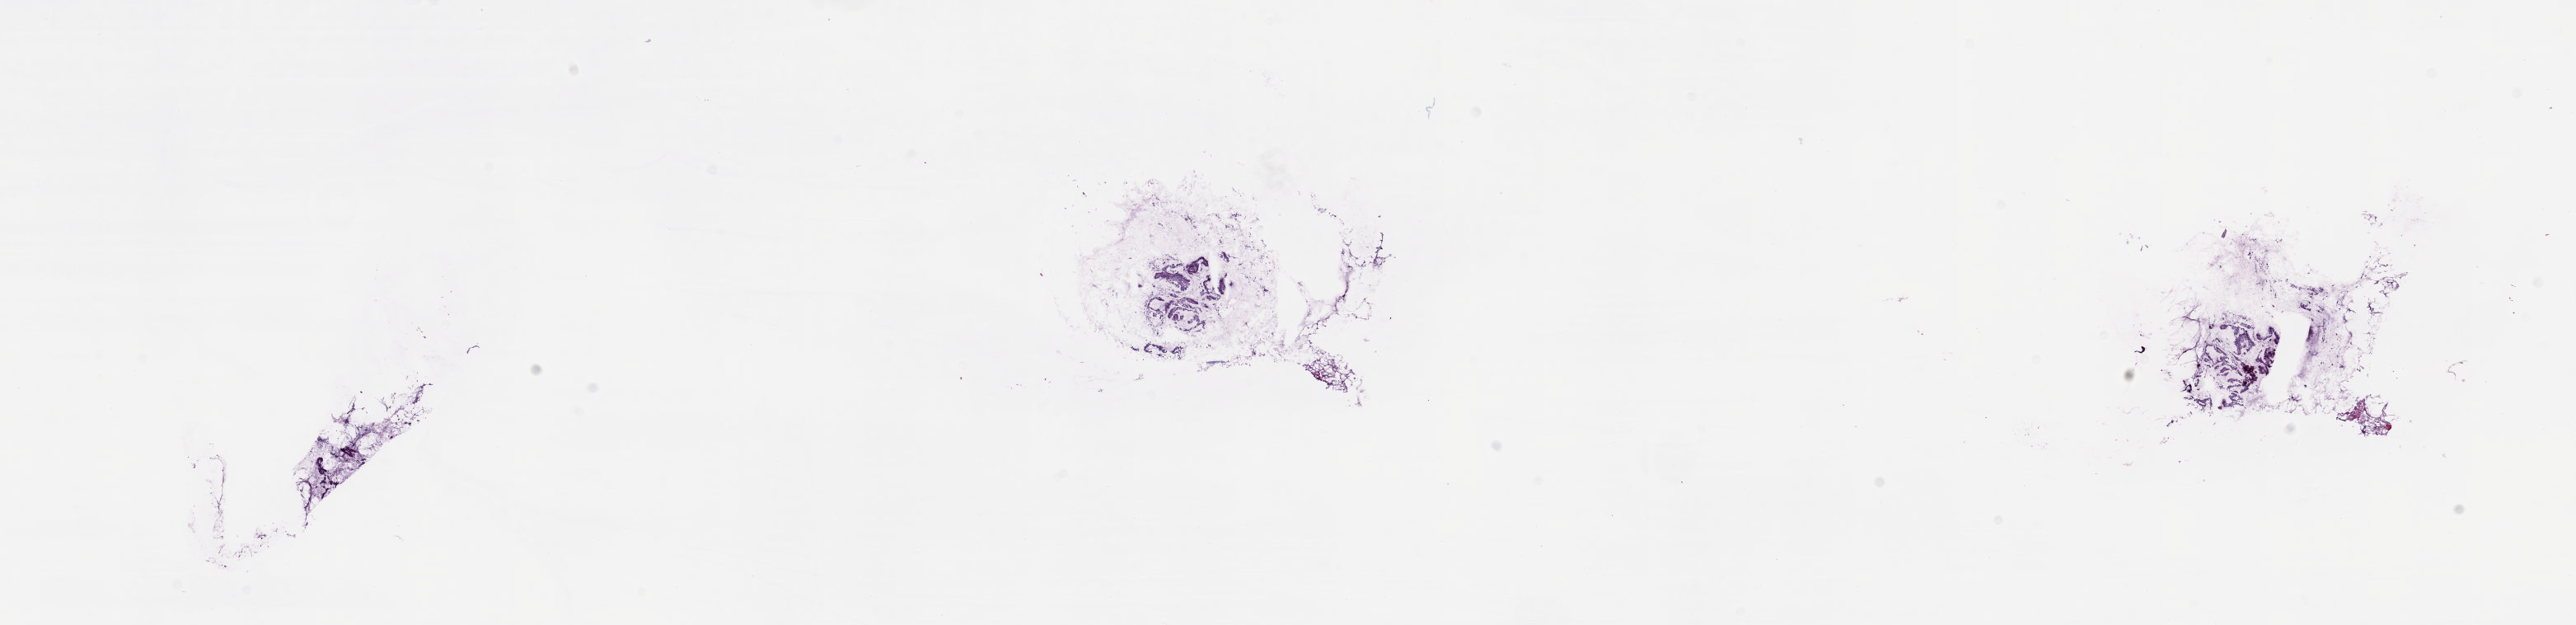
Digitized H&E tissue section (whole slide) — low-resolution overview of the scanned area, about 24.8 x 6.0 mm (acquisition: 20x scan). Frozen section. Sample: solid tissue normal (non-tumour tissue), esophagus. Male patient; age at initial diagnosis 77 years. Slide review estimates, as recorded: tumour cells 0%, tumour nuclei 0%, normal cells 100%, stromal cells 0%, necrosis 0%. Infiltration values recorded for this section: lymphocyte infiltration 0%, monocyte infiltration 1%, neutrophil infiltration 0%.
• this section: solid tissue normal sample (biorepository sample class)
• patient diagnosis: Adenocarcinoma, NOS (lower third of esophagus)